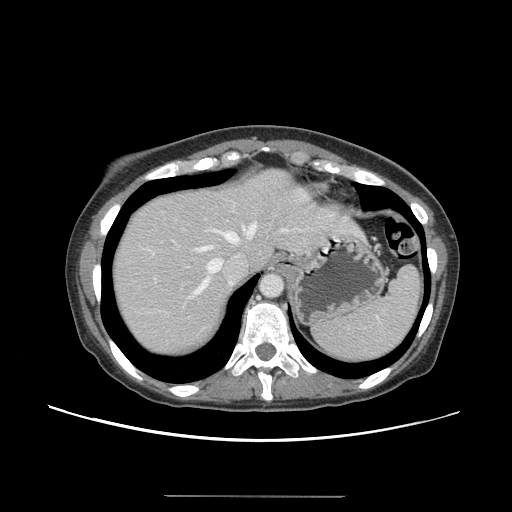
Contrast-enhanced abdominal CT, one axial slice; position 120 of 144 along the scan axis; 120 kVp; soft-tissue window (W 400 / L 40 HU); 2.5 mm slice thickness; 512 × 512 image matrix, field of view 380 × 380 mm. Female patient, age 53 years. From the clinical record (not read from this slice): diagnosis: colorectal cancer liver metastases, imaged before liver resection; multiple liver metastases: yes; largest metastasis: 1.1 cm; chemotherapy before resection: no.
Annotated regions visible in this slice (expert manual segmentation):
- hepatic veins: bounding box (x1, y1, x2, y2) in pixels: (189, 223, 287, 298)
- liver: (112, 171, 359, 356)
- planned liver remnant (the part of the liver to remain after resection): (112, 170, 285, 297)